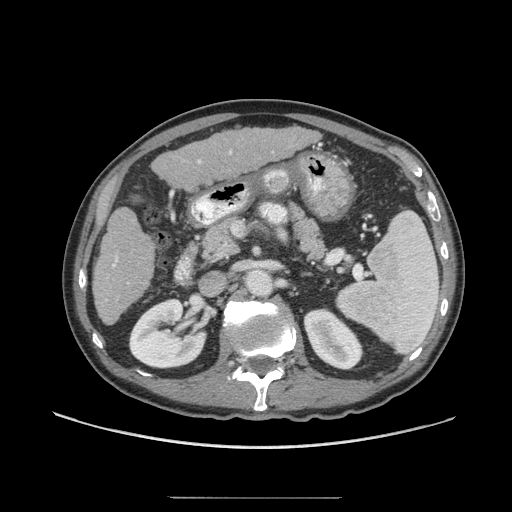
Contrast-enhanced abdominal CT (liver protocol), one axial slice. Slice 26 of 71 in the series (ordered by position). Reconstruction kernel STANDARD. Soft-tissue window (W 400 / L 40 HU). 2.5 mm slice thickness. 512 × 512 image matrix, field of view 400 × 400 mm. From the clinical record (not read from this slice): diagnosis: hepatocellular carcinoma (patient treated with transarterial chemoembolisation; whether this scan precedes or follows treatment is not stated here); TNM stage (as recorded): Stage-I; Child-Pugh class: A; tumour differentiation: well differentiated; tumour nodularity: uninodular.
Annotated regions visible in this slice (semi-automatic segmentation, software-assisted and operator-edited):
- liver parenchyma outside the tumour (the mass and vessels are separate outlines, so this box may not span the whole liver): bounding box [x1, y1, x2, y2] px = [92, 126, 314, 324]
- liver vessels: [106, 256, 129, 300]